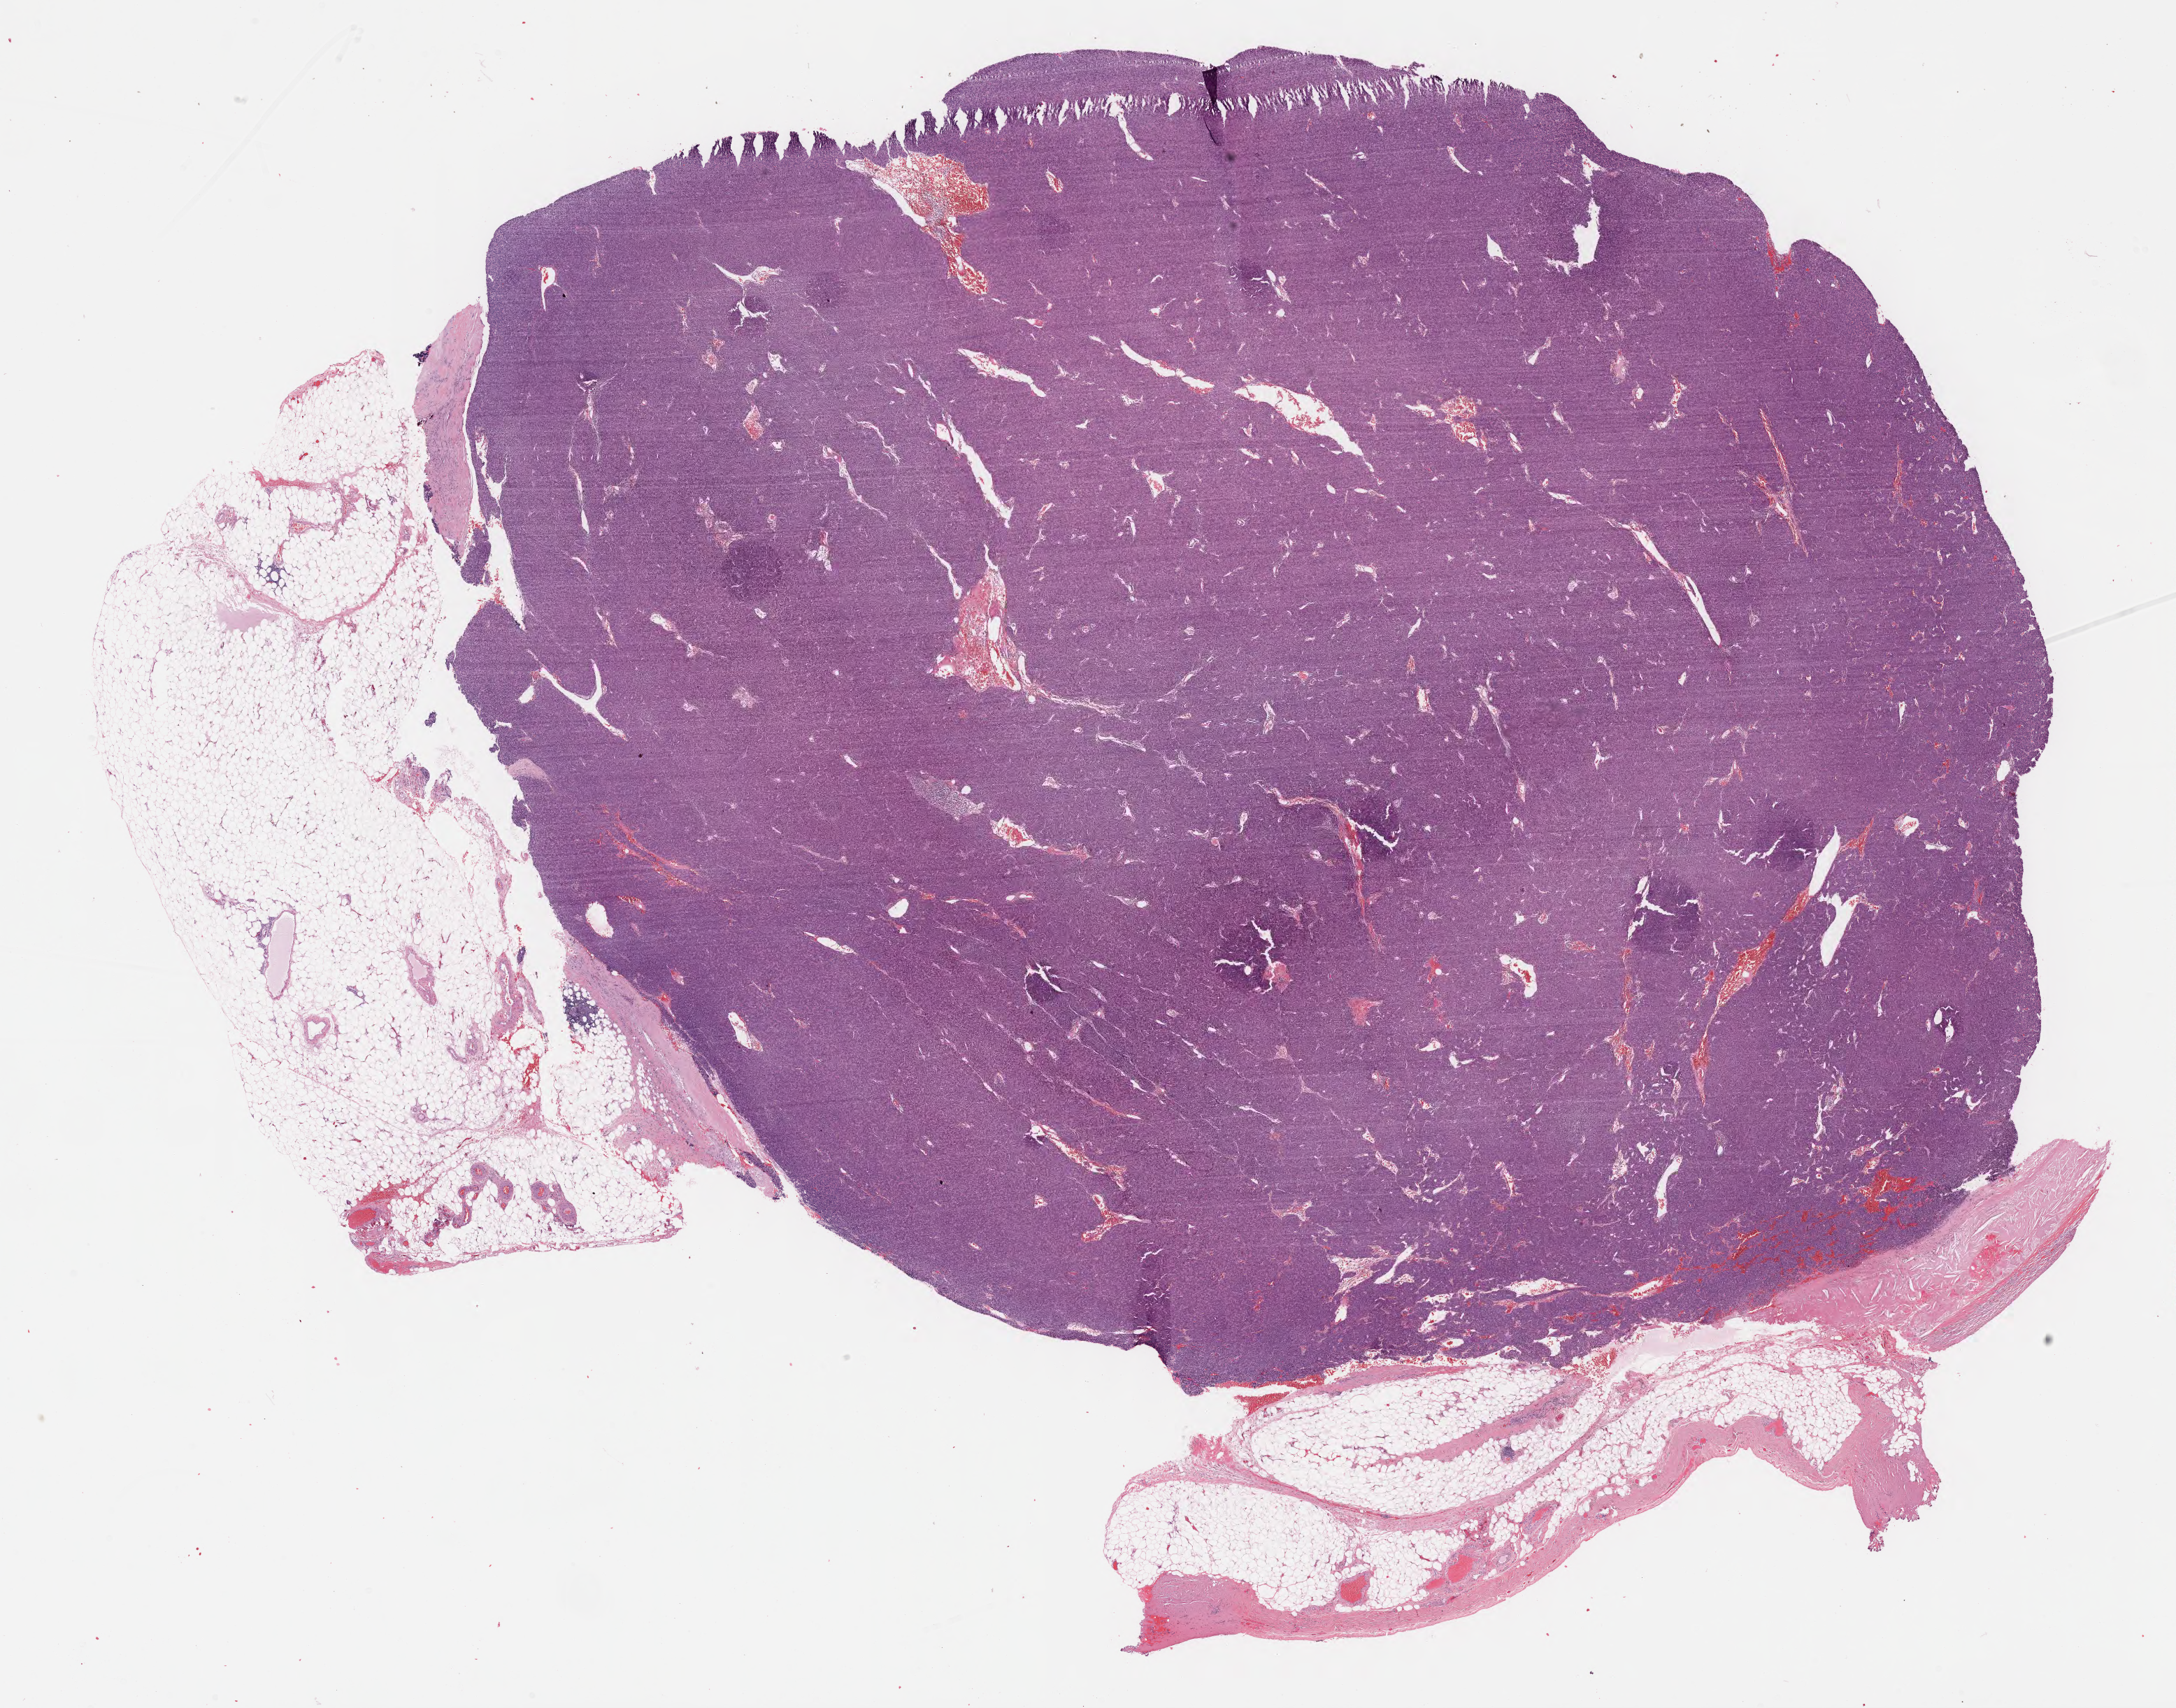
H&E whole-slide image, low-resolution overview of the scanned area, about 25.1 x 19.7 mm (acquisition: 40x scan), formalin-fixed paraffin-embedded (FFPE) diagnostic section, sample: primary tumour, thymus. Female, age 76 years at initial diagnosis.
Pathologic diagnosis: Thymoma, type A, malignant.